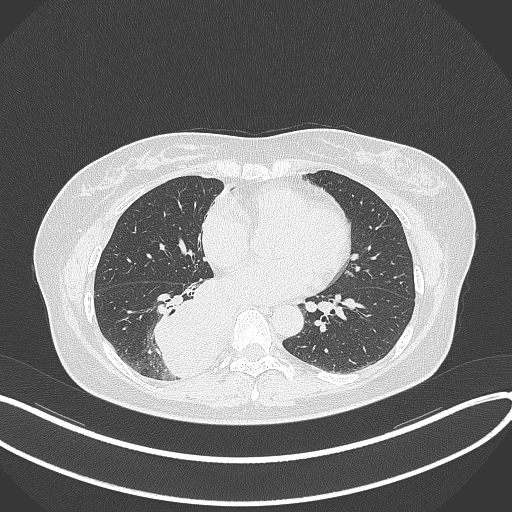
Chest CT, one axial slice; slice 151 of 331 in the series (ordered by position); lung window (W 1500 / L -600 HU); 1 mm slice thickness; 512 × 512 image matrix, field of view 400 × 400 mm. Patient: female, 54 years. Case-level facts recorded for this patient, not image findings: clinical TNM (as recorded): T4 N0 M0.
Structures marked on this image (bounding box drawn by a radiologist):
- lung tumour (recorded histology: adenocarcinoma): bounding box [x1, y1, x2, y2] px = [150, 286, 228, 379]